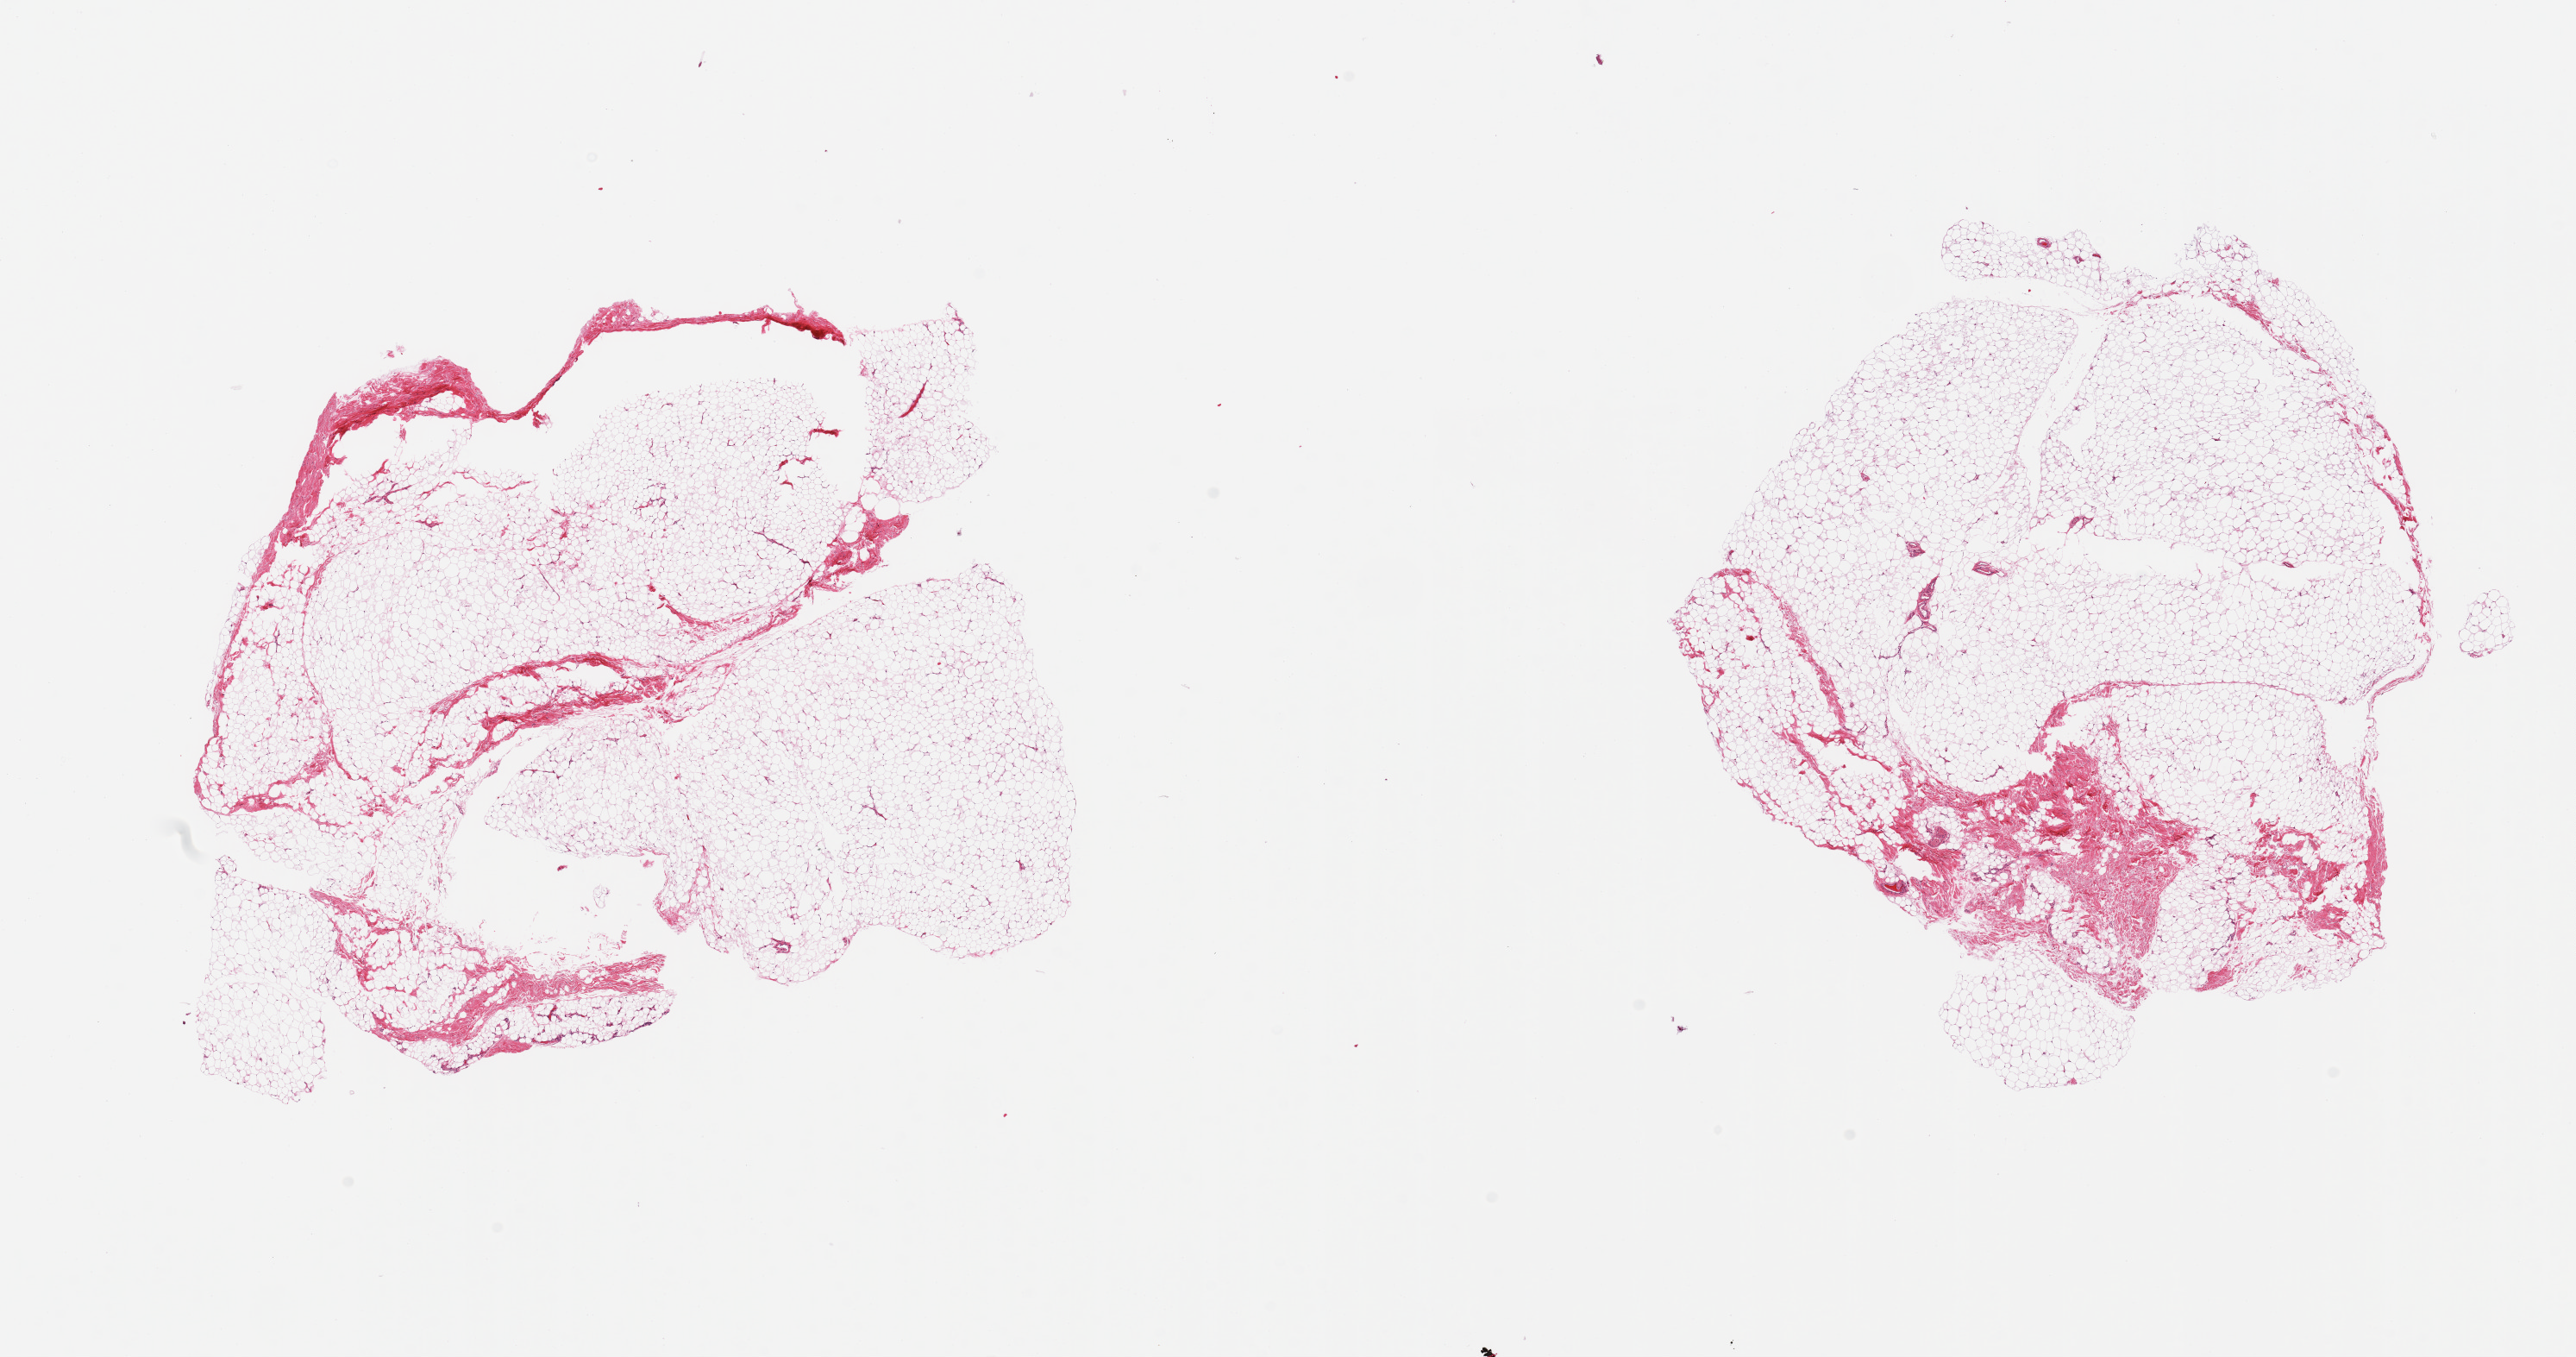
Digitized haematoxylin and eosin-stained section, whole scanned area (about 23.6 x 12.4 mm) shown as a low-resolution overview; PAXgene-fixed paraffin-embedded (PFPE) section; target tissue: breast; donor tissue sample. Donor: male.
Review note (as recorded): 2 pieces; 90% fat, 10% fibrous; no mammary ducts.